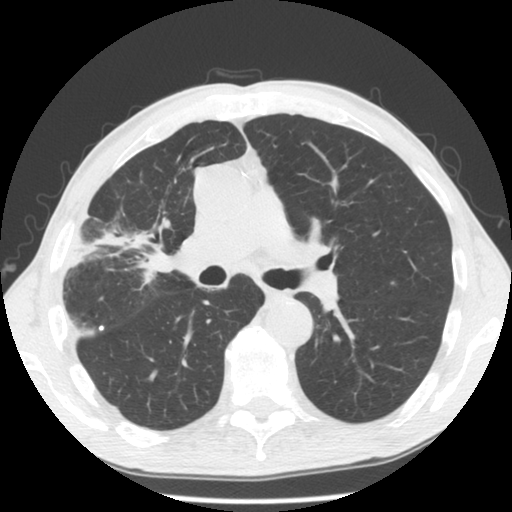
Low-dose screening chest CT, one axial slice. Slice 78 of 132 in the series (ordered by position). Lung window (W 1500 / L -600 HU). 512 × 512 image matrix, field of view 334 × 334 mm.
Structures marked on this image (outlined manually by an expert reader):
- lesion 1 (tumor, hilum of right lung): box from (x=137, y=240) to (x=172, y=275) px